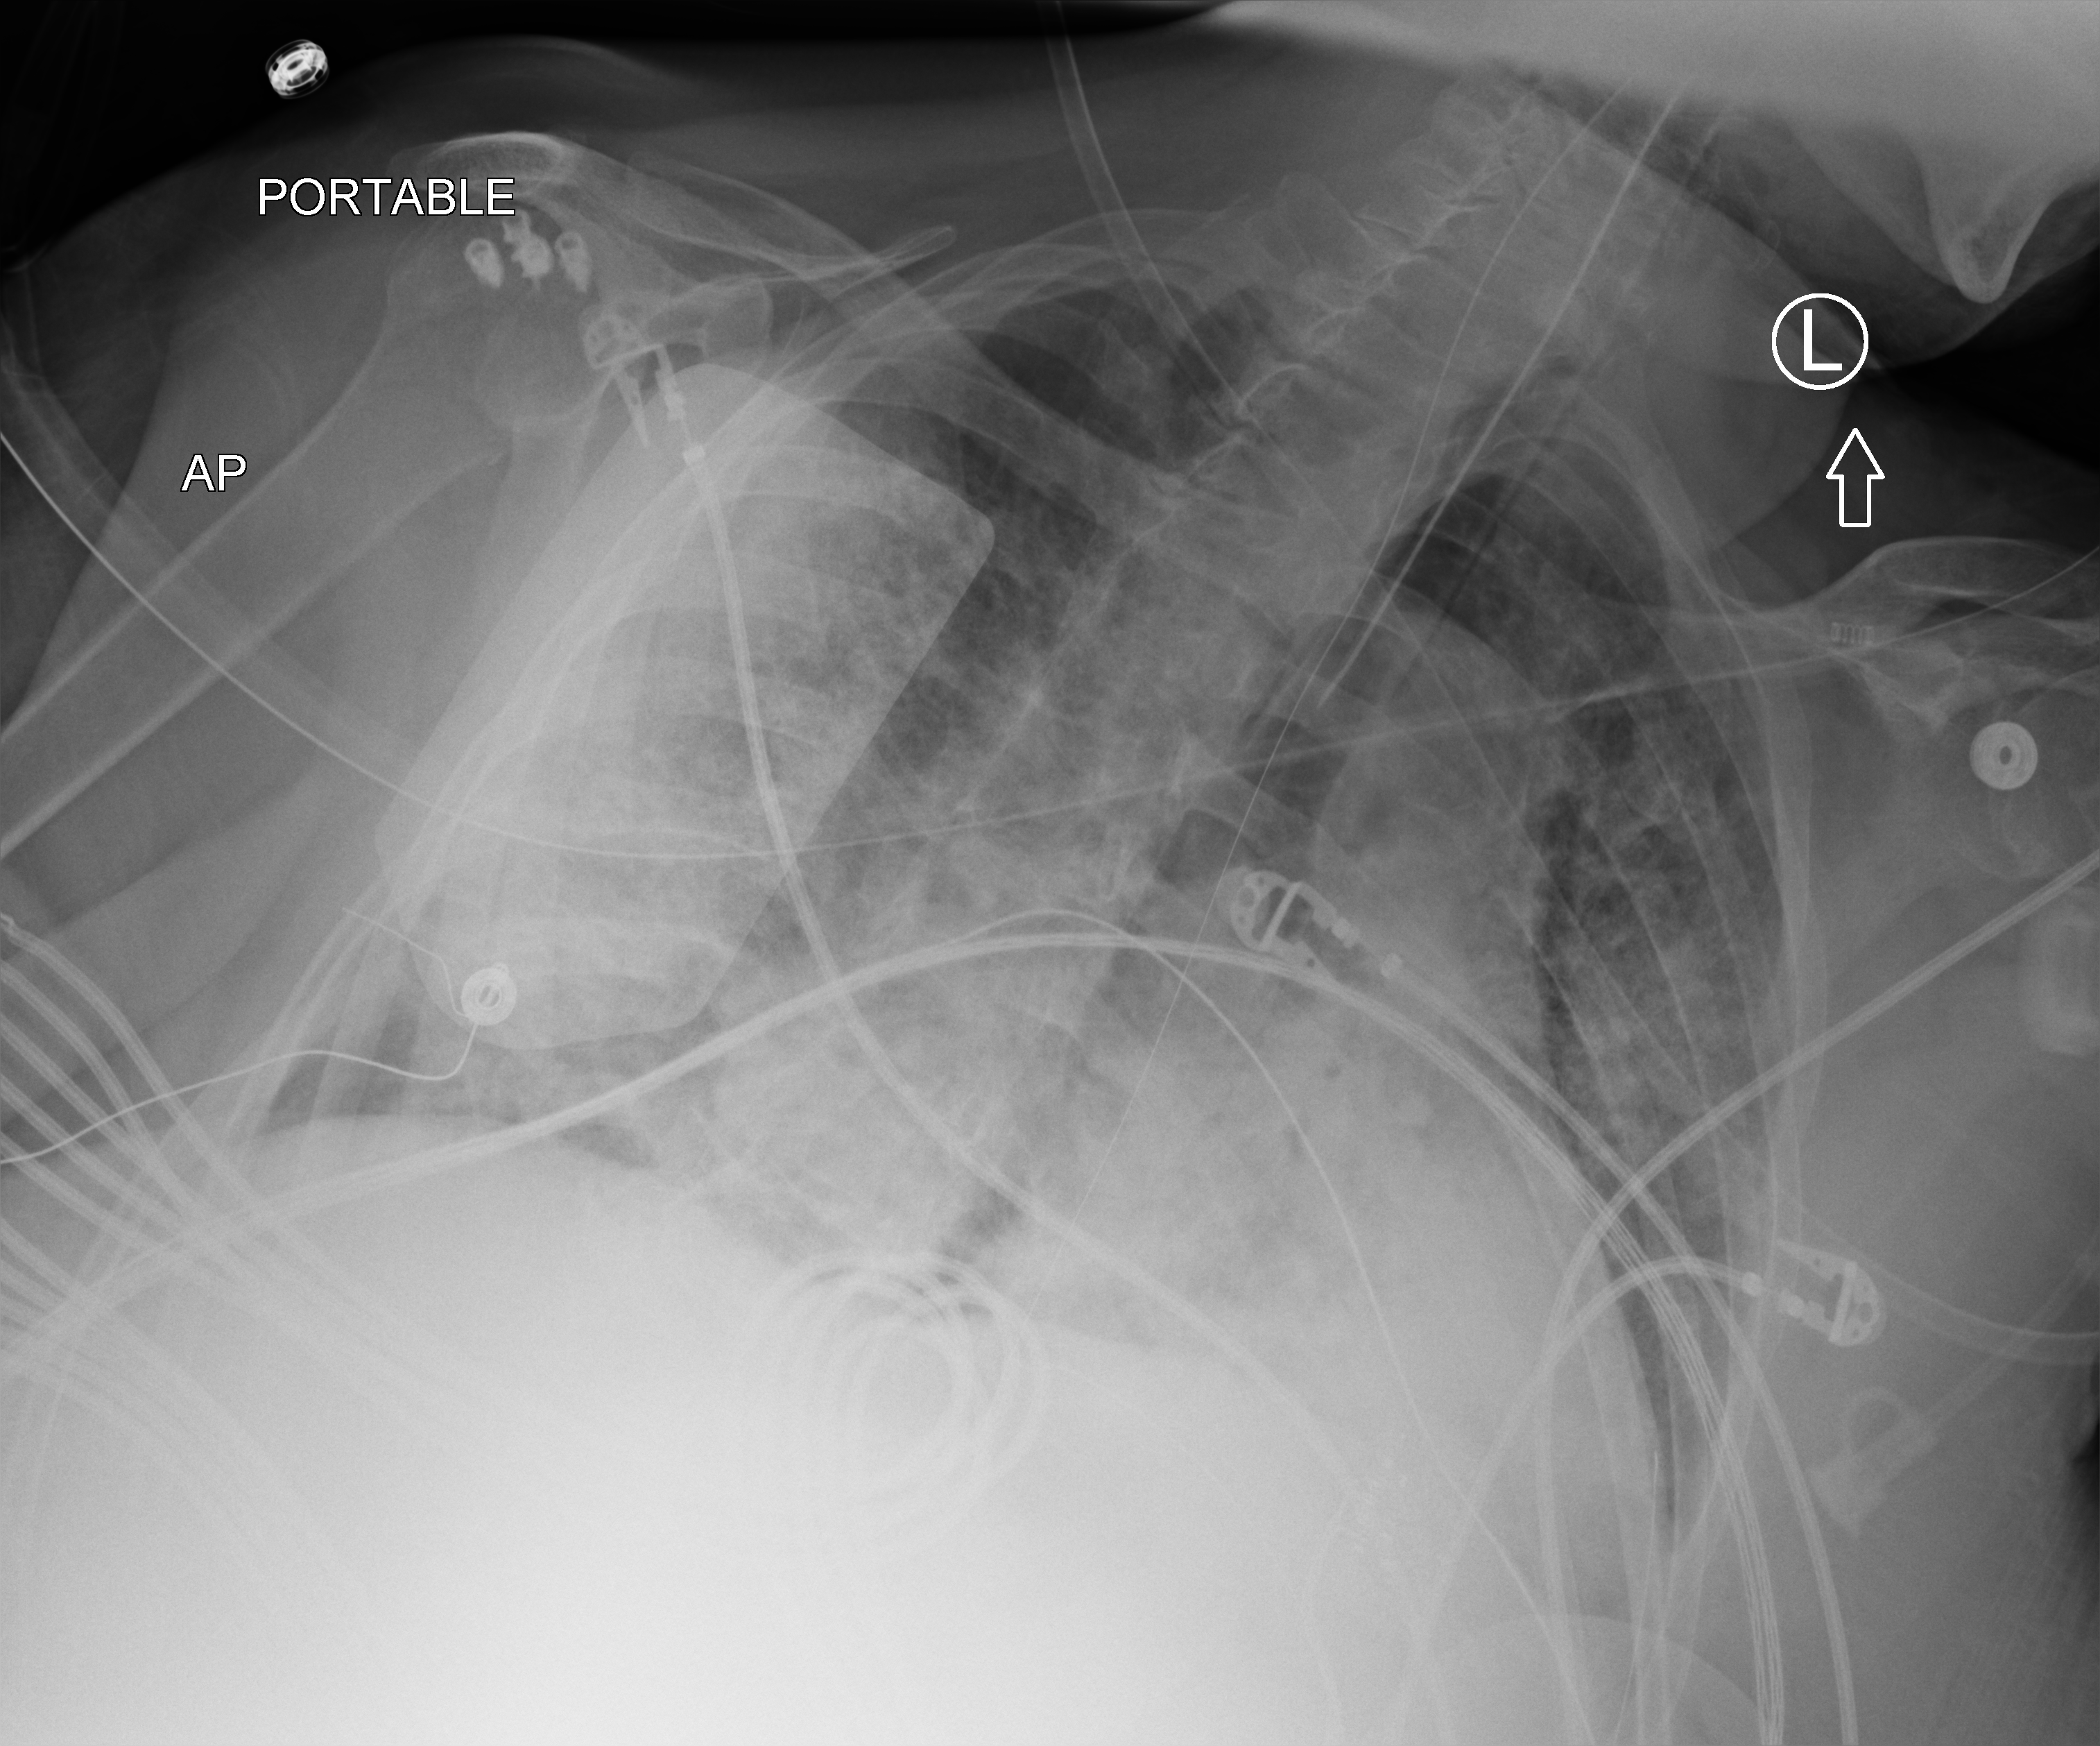
Bedside chest radiograph (computed radiography); anteroposterior (AP) projection. Female patient hospitalised with COVID-19, age 60–74 years.
From the hospital-stay record, not from the radiograph (when in the stay this image was taken is not recorded):
- admitted to intensive care during this hospital stay: yes
- mechanically ventilated during this hospital stay: yes